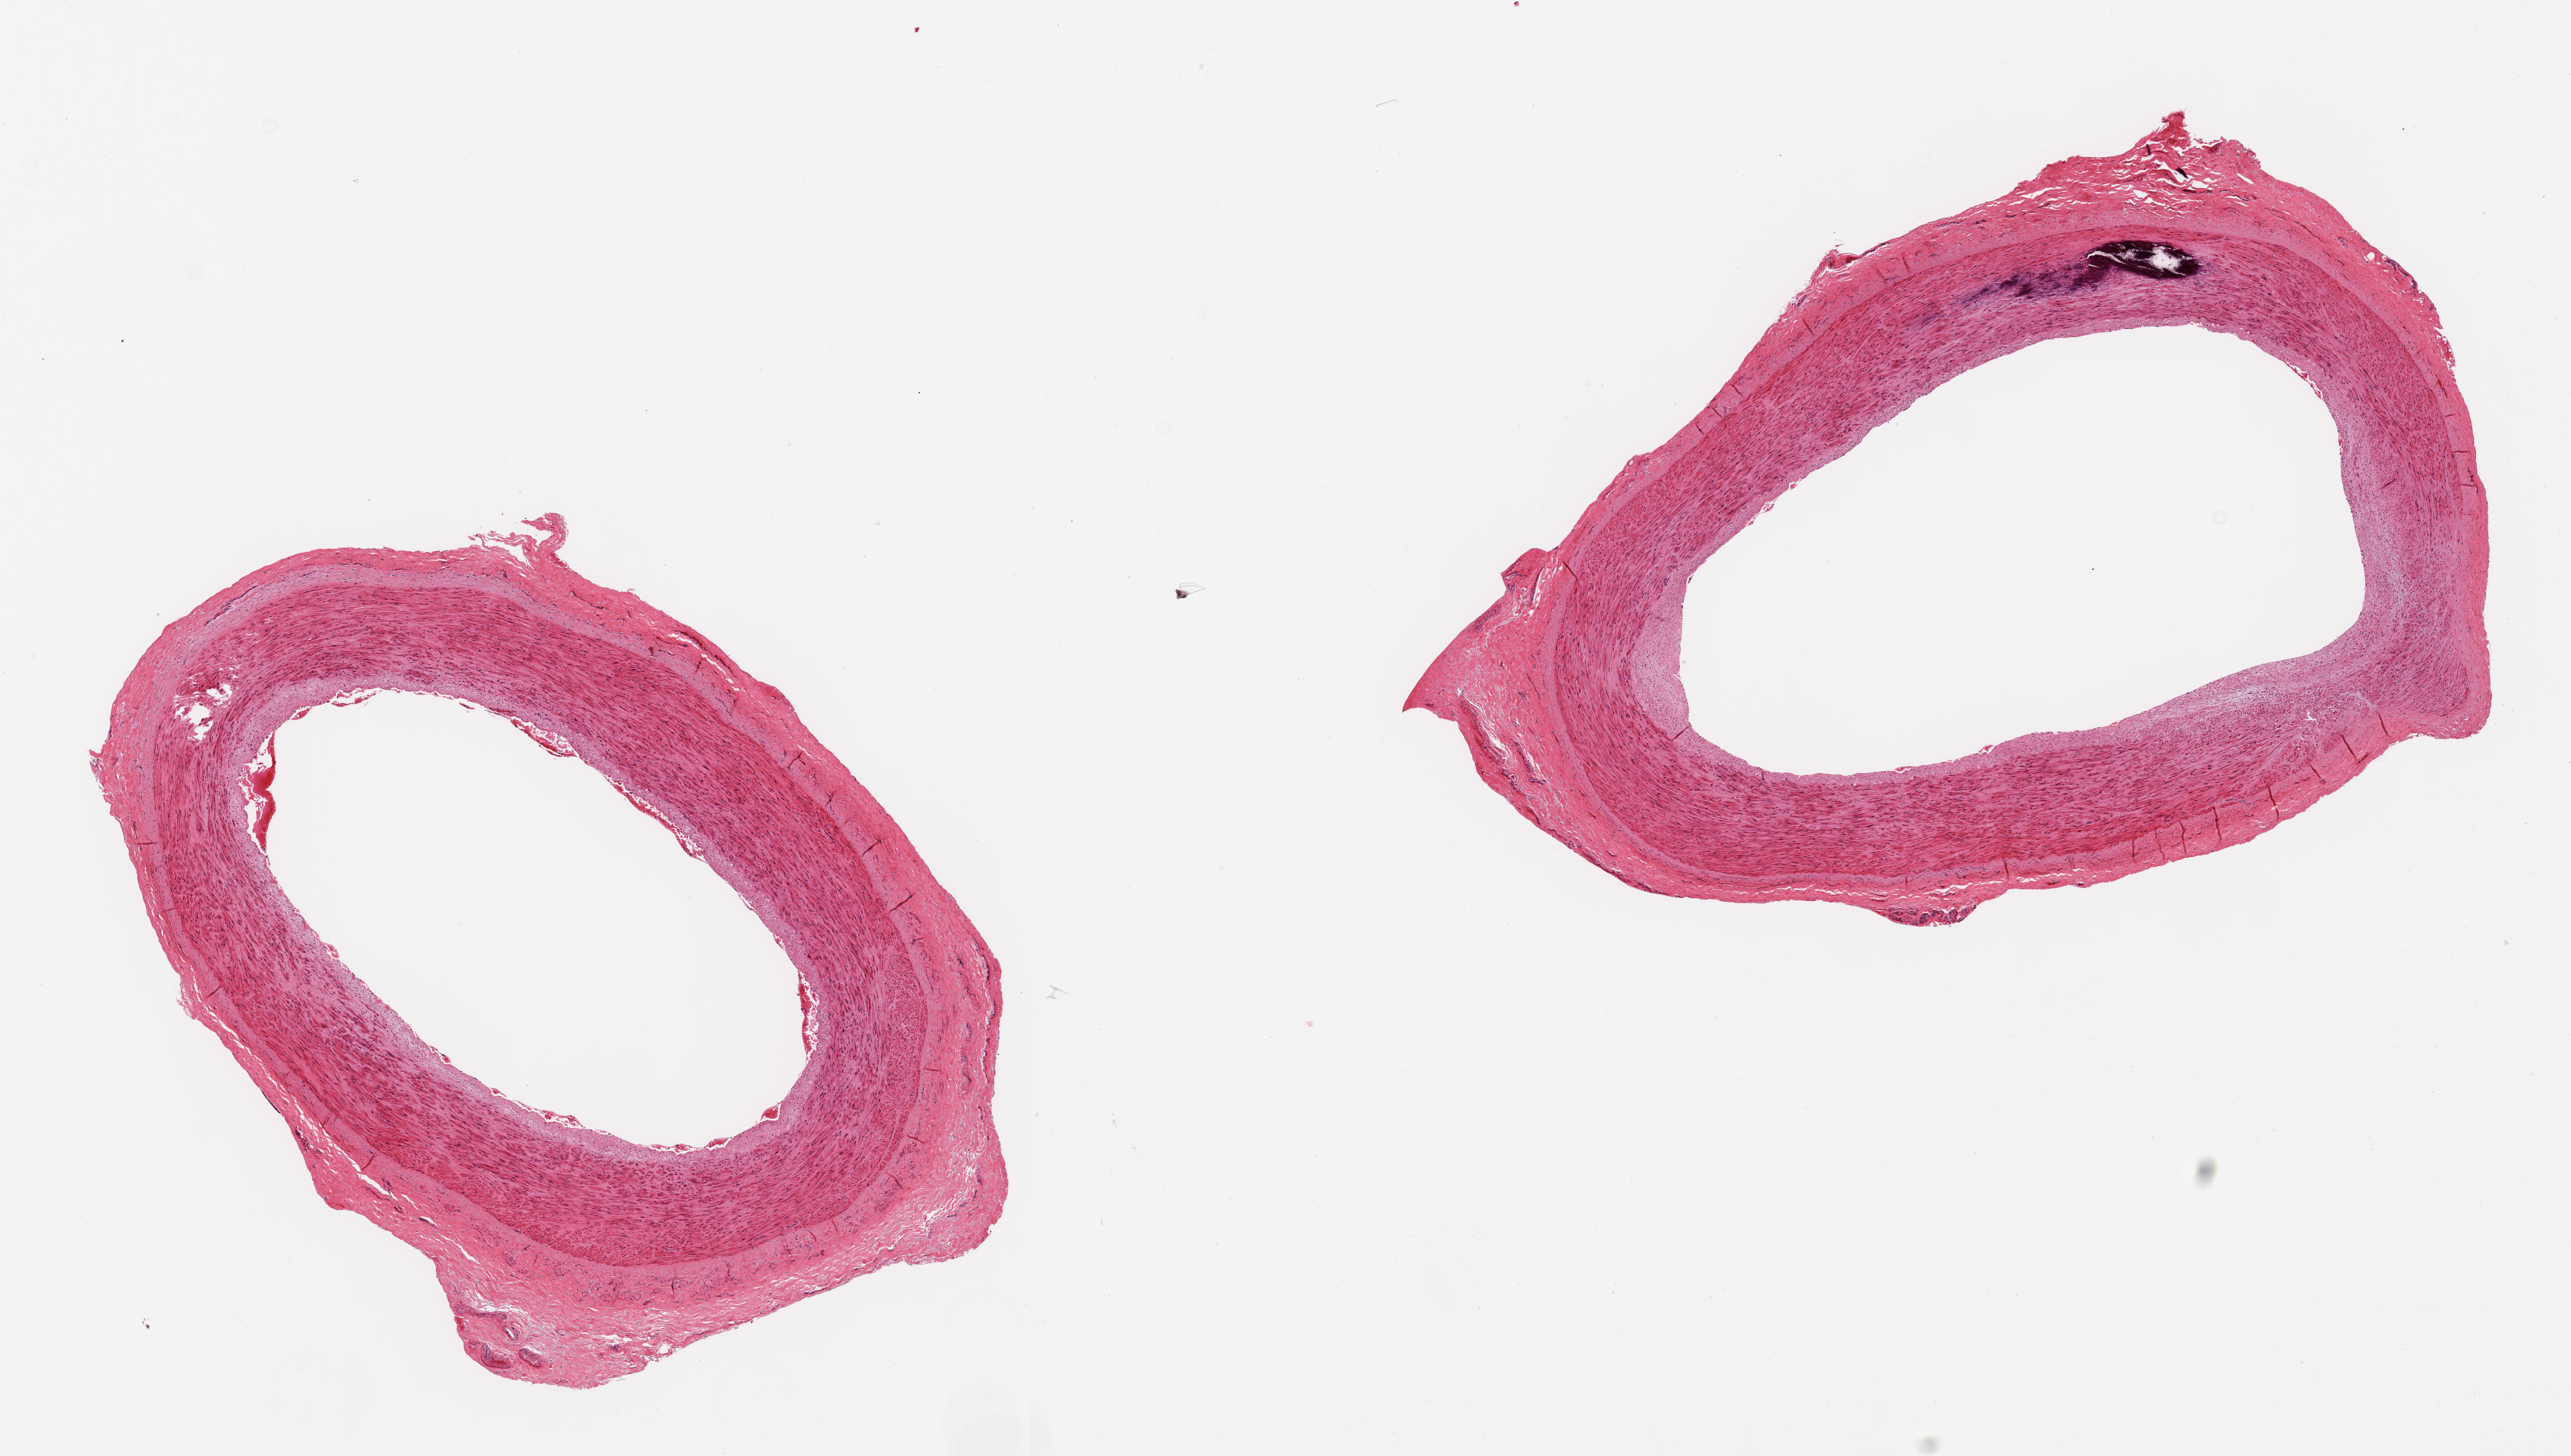
Whole-slide image, H&E stain — whole scanned area (about 14.8 x 8.4 mm) shown as a low-resolution overview. PAXgene-fixed, paraffin-embedded tissue. Section of tibial artery (target tissue). Tissue donor sample.
* review note (as recorded): 2 pieces, focal Monckeberg medial sclerosis; minmal atherosis or adherent fat